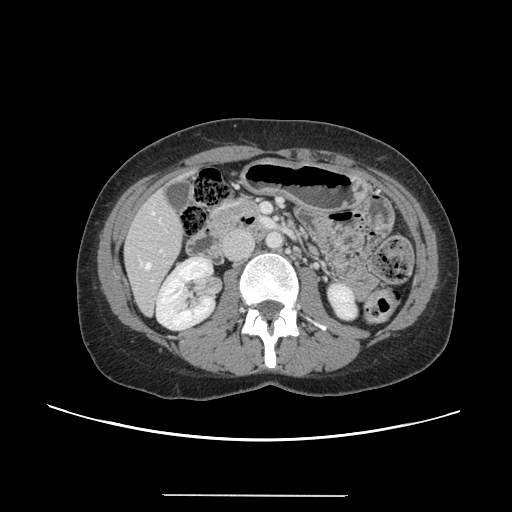
Contrast-enhanced abdominal CT, one axial slice. Position 48 of 144 along the scan axis. Intravenous contrast given. Soft-tissue window (W 400 / L 40 HU). 2.5 mm slice thickness. 512 × 512 image matrix, field of view 380 × 380 mm. Female patient, age 53 years. From the clinical record (not read from this slice): diagnosis: colorectal cancer liver metastases, imaged before liver resection; multiple liver metastases: yes; largest metastasis: 1.1 cm; disease in both lobes: no.
Outlined on this slice (outlined manually by an expert reader):
- hepatic veins: box from (x=146, y=212) to (x=155, y=269) px
- liver: (x=126, y=193)–(x=183, y=314)
- planned liver remnant (the part of the liver to remain after resection): (x=126, y=193)–(x=184, y=314)
- portal vein (with intrahepatic branches): (x=151, y=249)–(x=163, y=282)